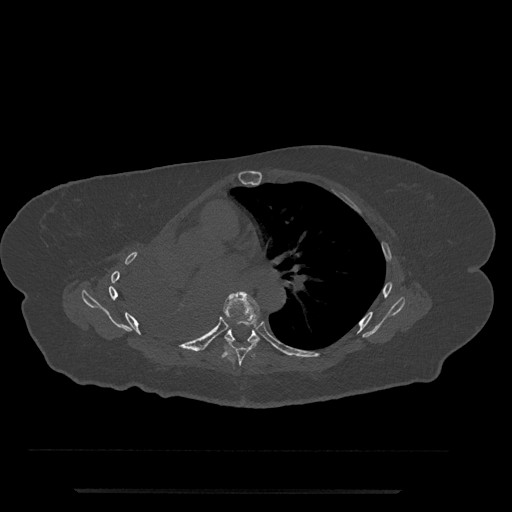
CT including the spine, one axial slice. Position 472 of 797 along the scan axis. Bone window (W 1800 / L 400 HU). 0.5 mm slice thickness. 512 × 512 image matrix, field of view 440 × 440 mm. Female patient, age 51 years. Case-level facts recorded for this patient, not image findings: primary cancer: neuro.
Outlined on this slice (semi-automatically segmented with operator editing):
- T6 vertebra: bounding box (x1, y1, x2, y2) in pixels: (223, 291, 260, 366)
- T7 vertebra: (224, 329, 260, 342)